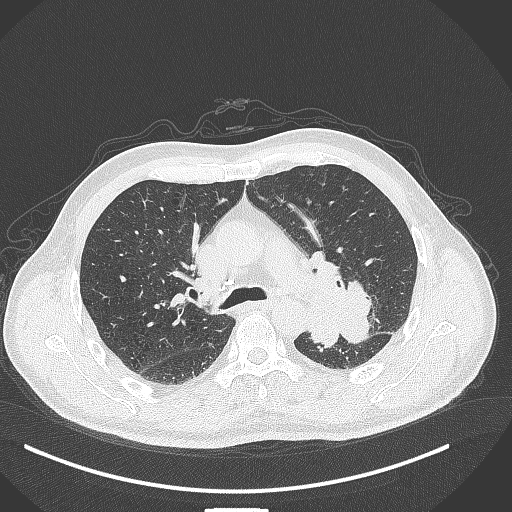
Chest CT, one axial slice; slice 275 of 429 in the series (ordered by position); 120 kVp; lung window (W 1500 / L -600 HU); 1 mm slice thickness; 512 × 512 image matrix, field of view 400 × 400 mm. Male patient, age 55 years. Case-level facts recorded for this patient, not image findings: clinical TNM (as recorded): T3 N0 M1c; histopathological grade: G3.
Outlined on this slice (rectangle marked by the reading radiologist):
- lung tumour (recorded histology: adenocarcinoma): box from (x=306, y=246) to (x=381, y=354) px